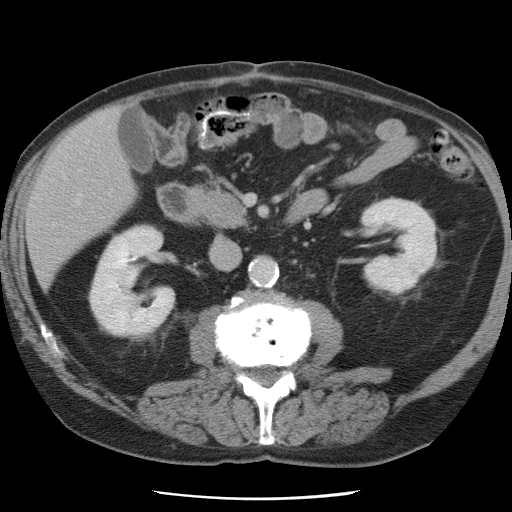
Contrast-enhanced abdominal CT, one axial slice. Position 26 of 78 along the scan axis. Intravenous contrast given. Soft-tissue window (W 400 / L 40 HU). 5 mm slice thickness. 512 × 512 image matrix, field of view 337 × 337 mm. Male patient, age 75 years. From the clinical record (not read from this slice): diagnosis: colorectal cancer liver metastases, imaged before liver resection; multiple liver metastases: yes; largest metastasis: 2.4 cm; disease in both lobes: yes.
Structures marked on this image (manually delineated by an expert):
- liver: bounding box (x1, y1, x2, y2) in pixels: (28, 108, 137, 284)
- planned liver remnant (the part of the liver to remain after resection): (28, 118, 137, 284)